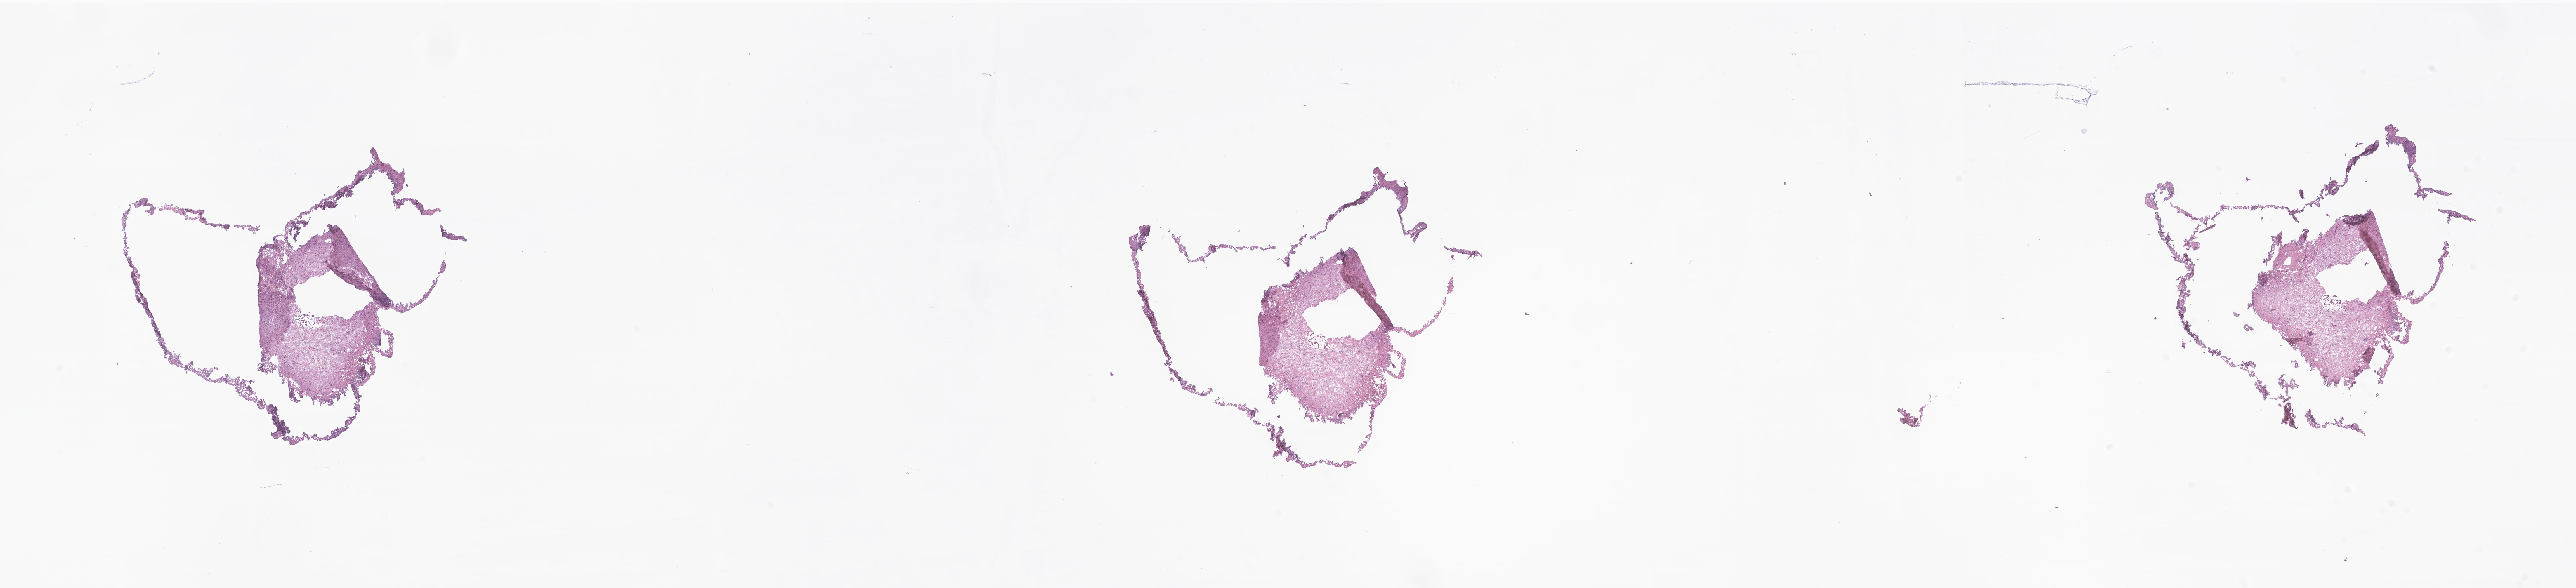
Whole-slide image, haematoxylin and eosin stain of tumor tissue from the spinal cord, low-resolution overview of the scanned area, about 38.8 x 8.9 mm. Cryosection (OCT / tissue freezing medium). Male patient, age 191 months.
Recorded diagnosis: Neurofibroma, NOS.